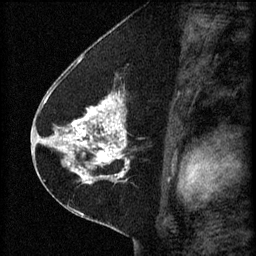
Breast MRI (dynamic contrast-enhanced), one sagittal slice. Slice 30 of 60 in the series (ordered by position). 3 images stored at this slice position (order not interpretable as contrast timing). 1.5 T. TE 4.2 ms, TR 8.2 ms. 2 mm slice thickness. 256 × 256 image matrix, field of view 180 × 180 mm. Female patient, age 41 years.
Structures marked on this image (semi-automatically segmented with operator editing):
- analysis volume of interest (the breast-tissue region the enhancement analysis was run in; not a lesion): bounding box <67,92,165,173> (left, top, right, bottom; pixels)
- tumour enhancement mask (voxels above the 70 % enhancement threshold inside the analysis volume of interest): <67,94,130,173>